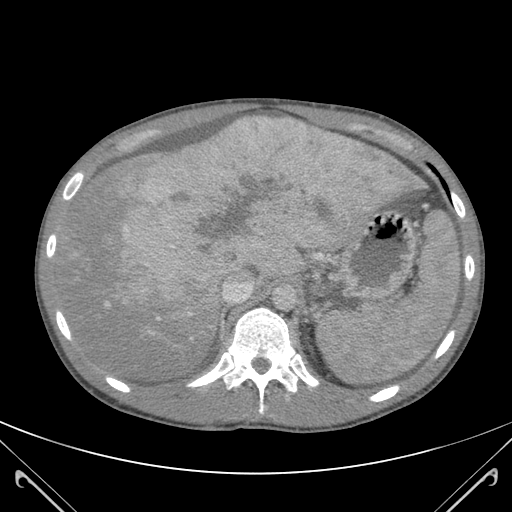
Contrast-enhanced abdominal CT (liver protocol), one axial slice. Position 86 of 118 along the scan axis. 120 kVp. Soft-tissue window (W 400 / L 40 HU). 512 × 512 image matrix. Case-level facts recorded for this patient, not image findings: diagnosis: hepatocellular carcinoma (patient treated with transarterial chemoembolisation; whether this scan precedes or follows treatment is not stated here); TNM stage (as recorded): Stage-IIIB; Child-Pugh class: A; tumour nodularity: uninodular.
Structures marked on this image (semi-automatically segmented with operator editing):
- abdominal aorta: bounding box [x1, y1, x2, y2] px = [272, 285, 298, 310]
- liver parenchyma outside the tumour (the mass and vessels are separate outlines, so this box may not span the whole liver): [60, 120, 422, 378]
- mass: [96, 122, 413, 326]
- liver vessels: [105, 120, 305, 339]